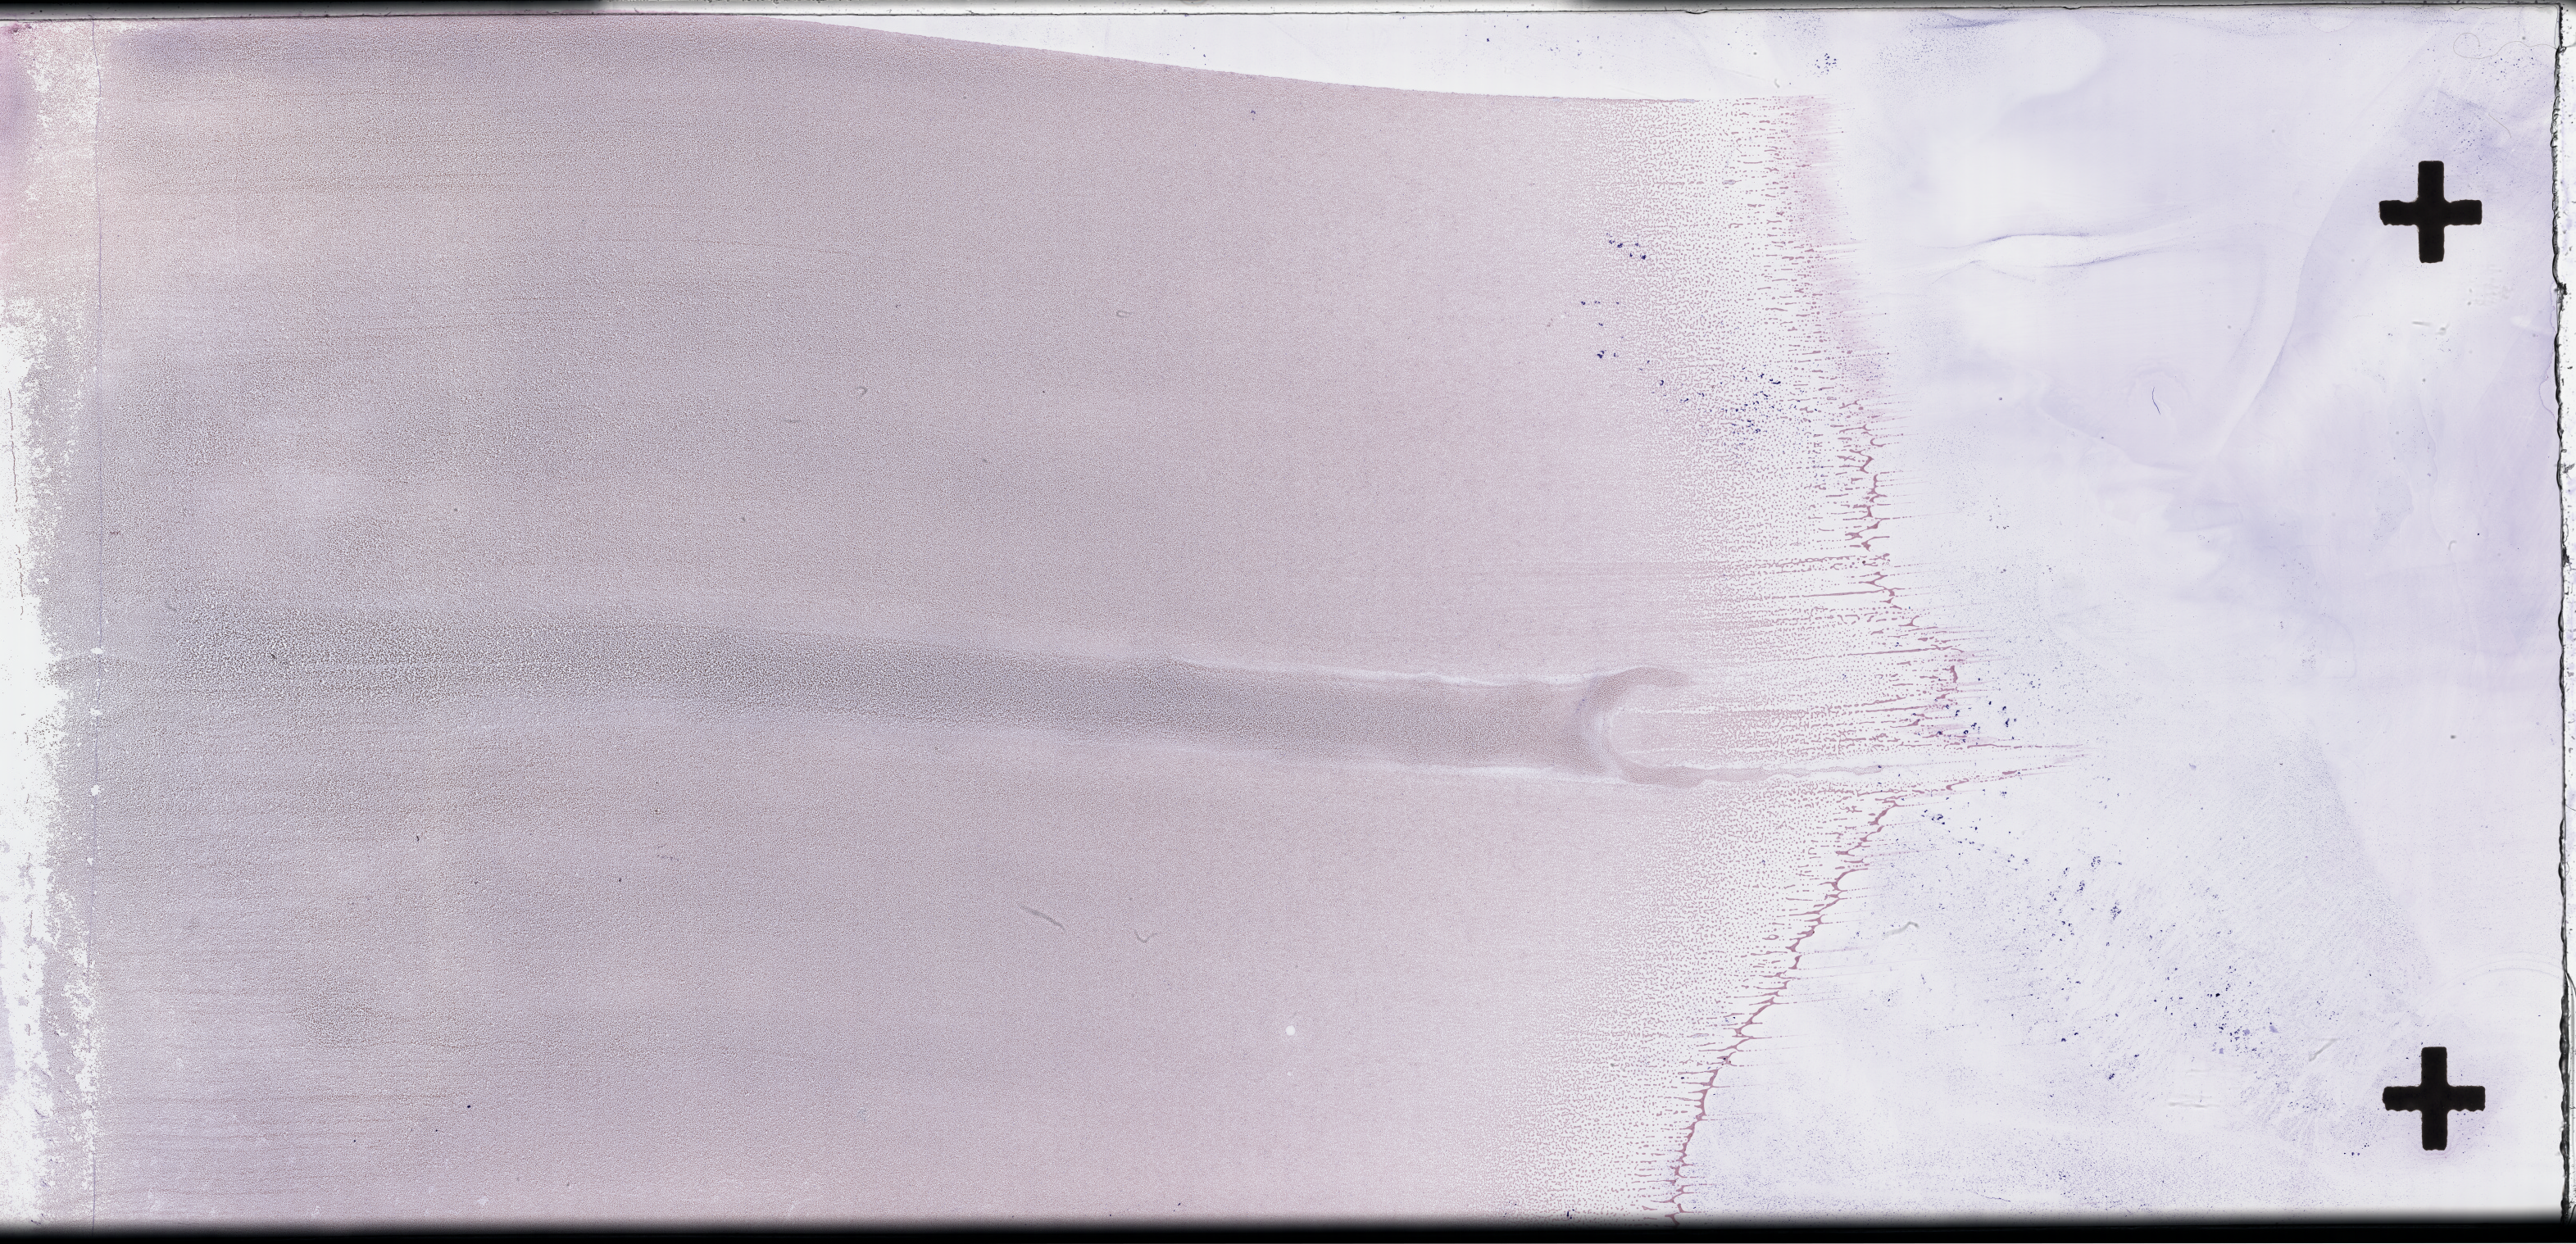
Wright–Giemsa-stained whole blood smear, whole-slide image, low-resolution overview of the scanned area, about 50.8 x 24.5 mm. EDTA-anticoagulated smear. Patient sex: female.
- from a patient with: Plasma Cell Myeloma